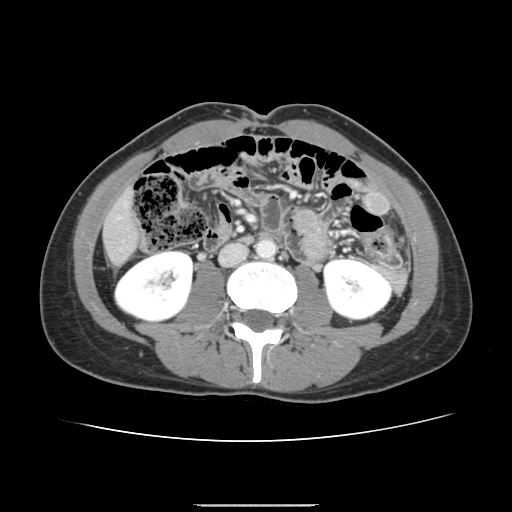
Contrast-enhanced abdominal CT, one axial slice; position 39 of 150 along the scan axis; intravenous contrast given; soft-tissue window (W 400 / L 40 HU); 2.5 mm slice thickness; 512 × 512 image matrix. Female patient, age 32 years. From the clinical record (not read from this slice): diagnosis: colorectal cancer liver metastases, imaged before liver resection.
Structures marked on this image (expert manual segmentation):
- liver: bounding box (x1, y1, x2, y2) in pixels: (105, 196, 137, 263)
- planned liver remnant (the part of the liver to remain after resection): (105, 196, 137, 263)